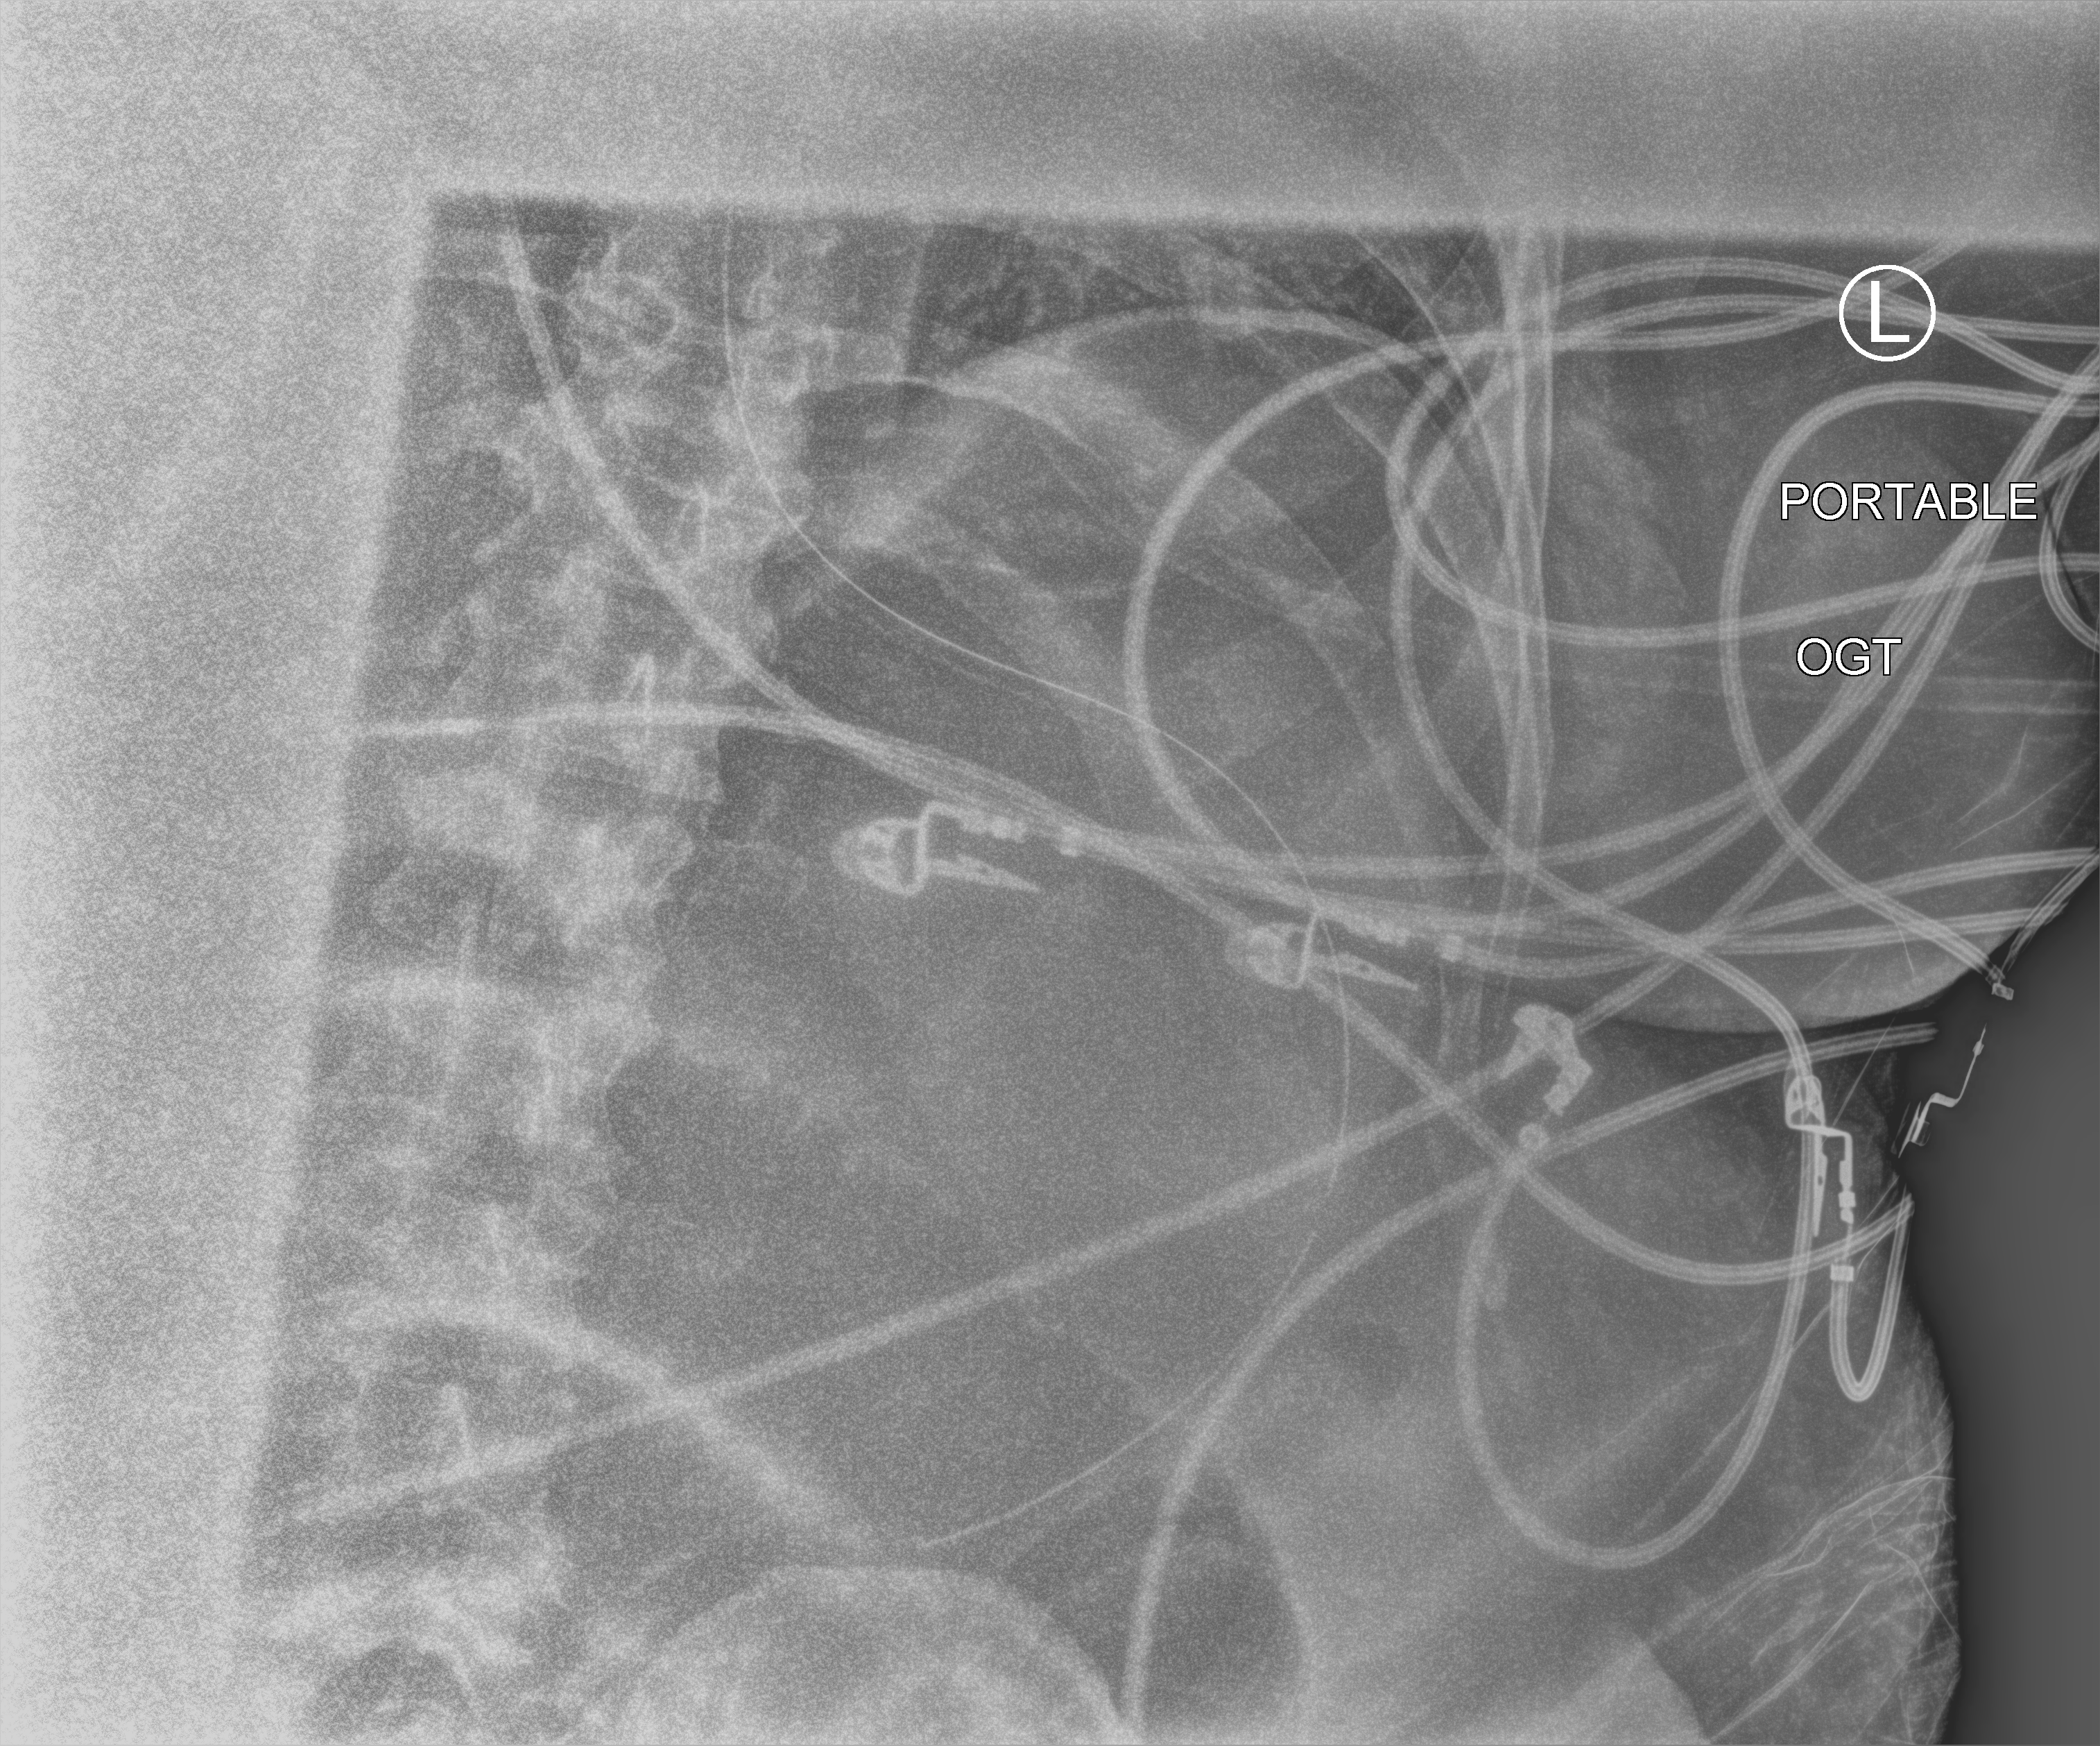
Portable chest radiograph. Patient hospitalised with COVID-19; male, aged 18–59 years.
Admission-level facts for this patient (not findings on this image; timing relative to this image not recorded):
- diabetes (admission record): yes